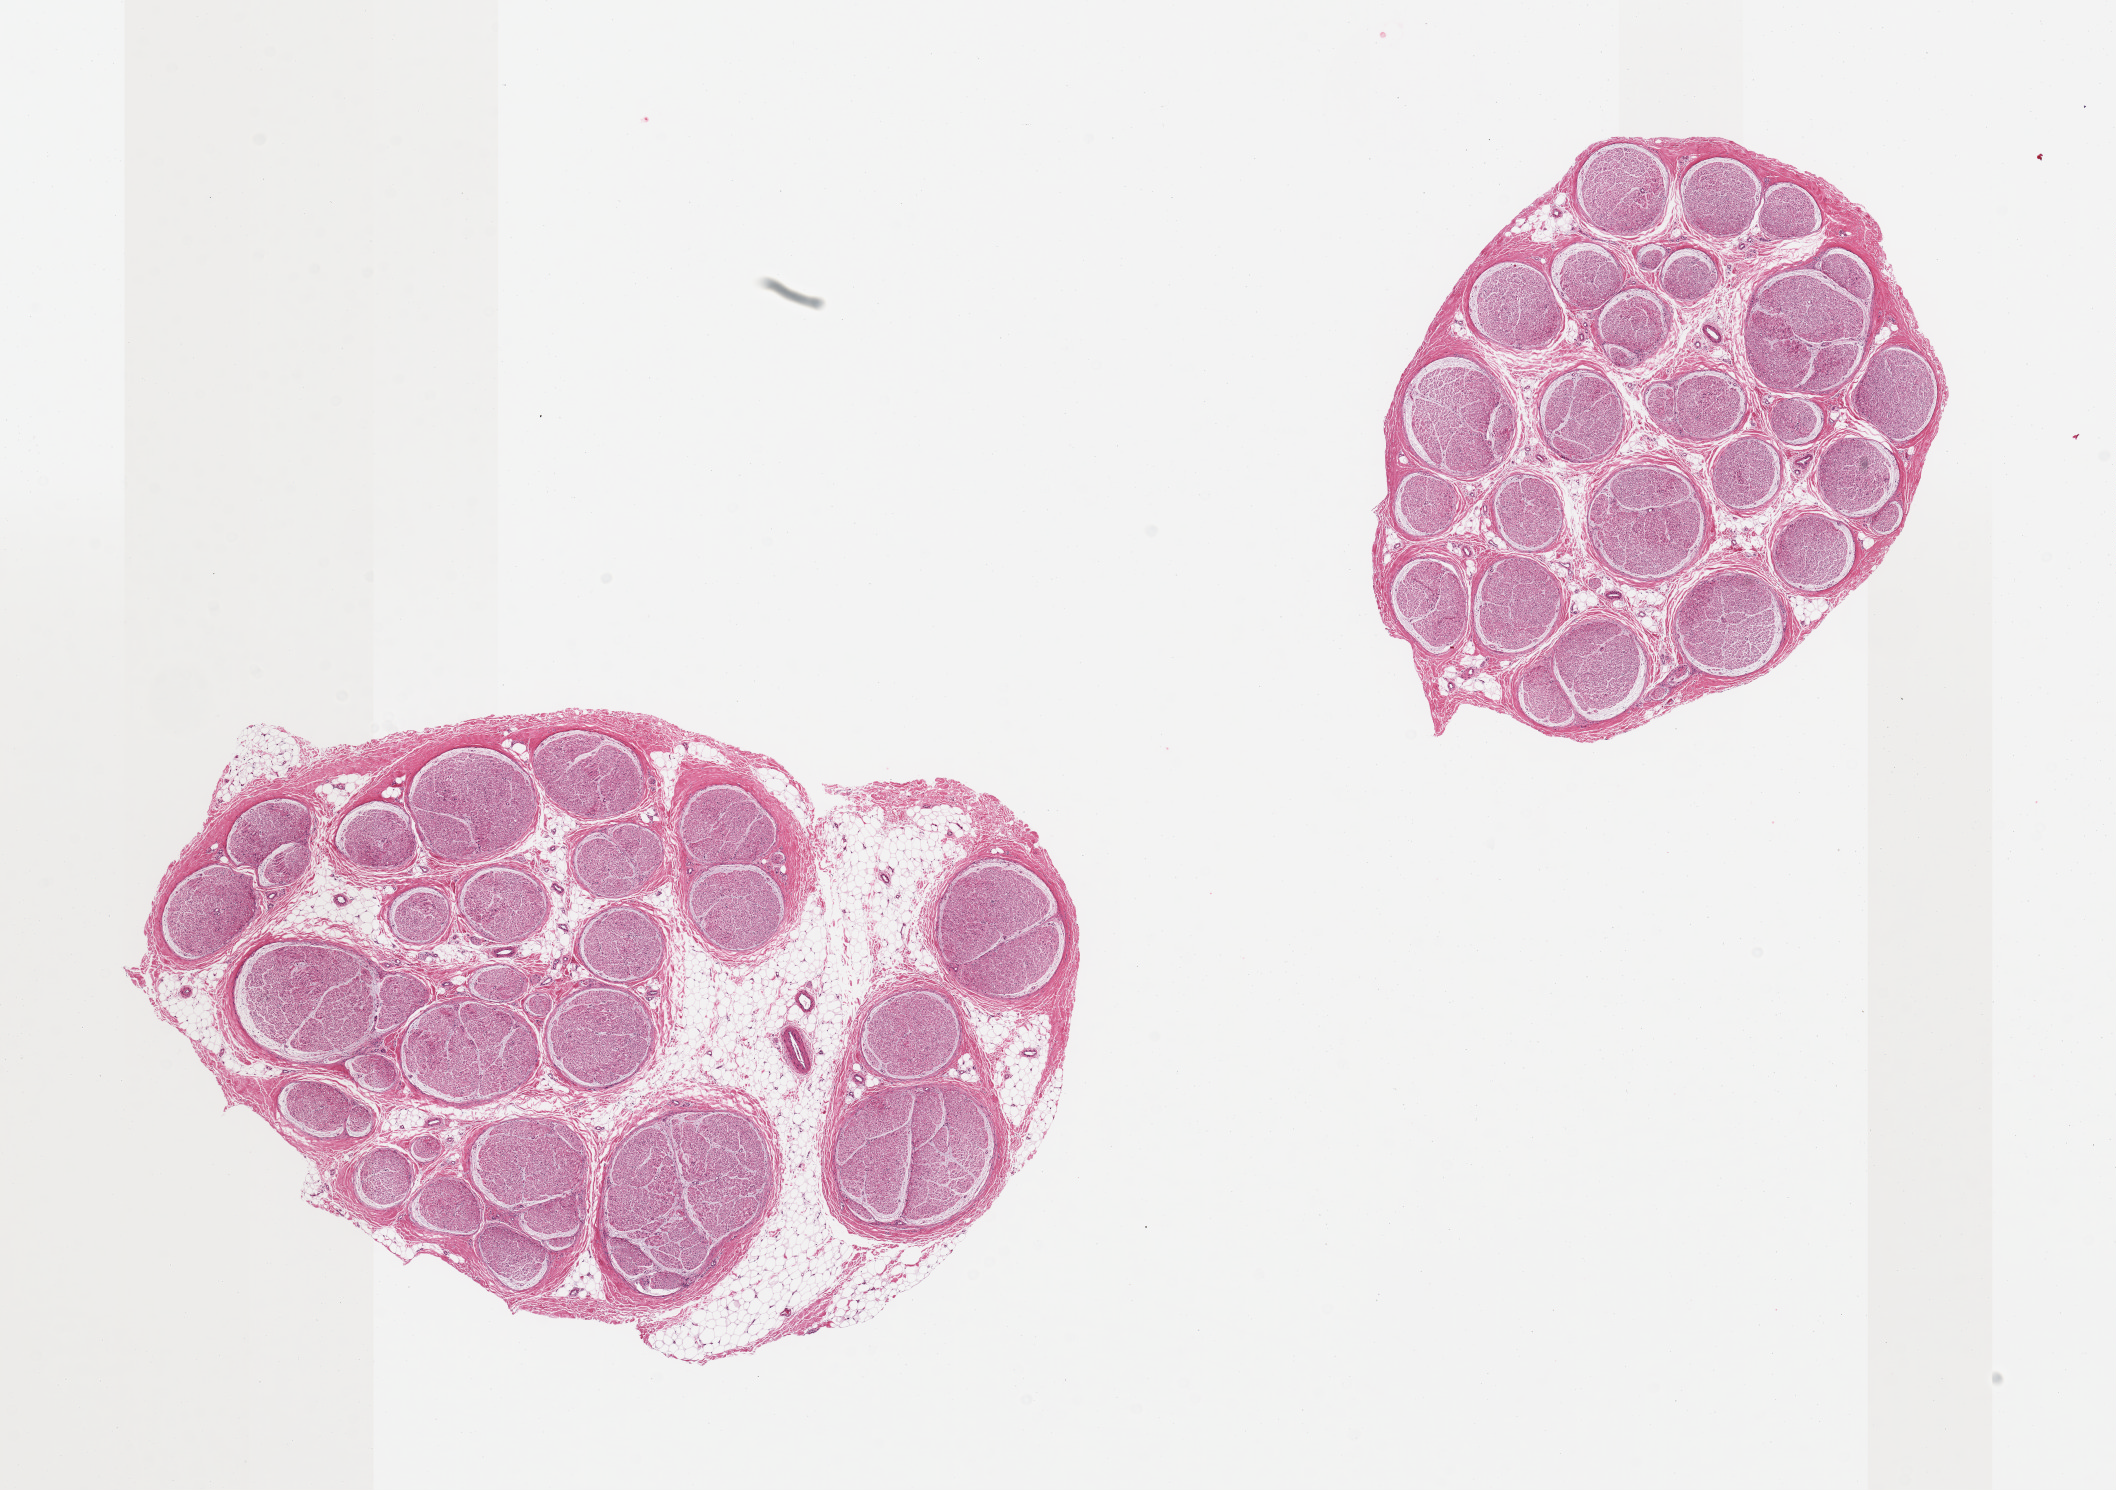
Whole-slide image, hematoxylin and eosin (H&E) stain, brightfield, whole scanned area (about 16.7 x 11.8 mm, acquisition: 20x scan) shown as a low-resolution overview; PAXgene-fixed paraffin-embedded (PFPE) section; section of tibial nerve (target tissue); donor tissue sample.
* pathologist's review note for this sample: 1 piece; nerve not artery; 20% internal fat